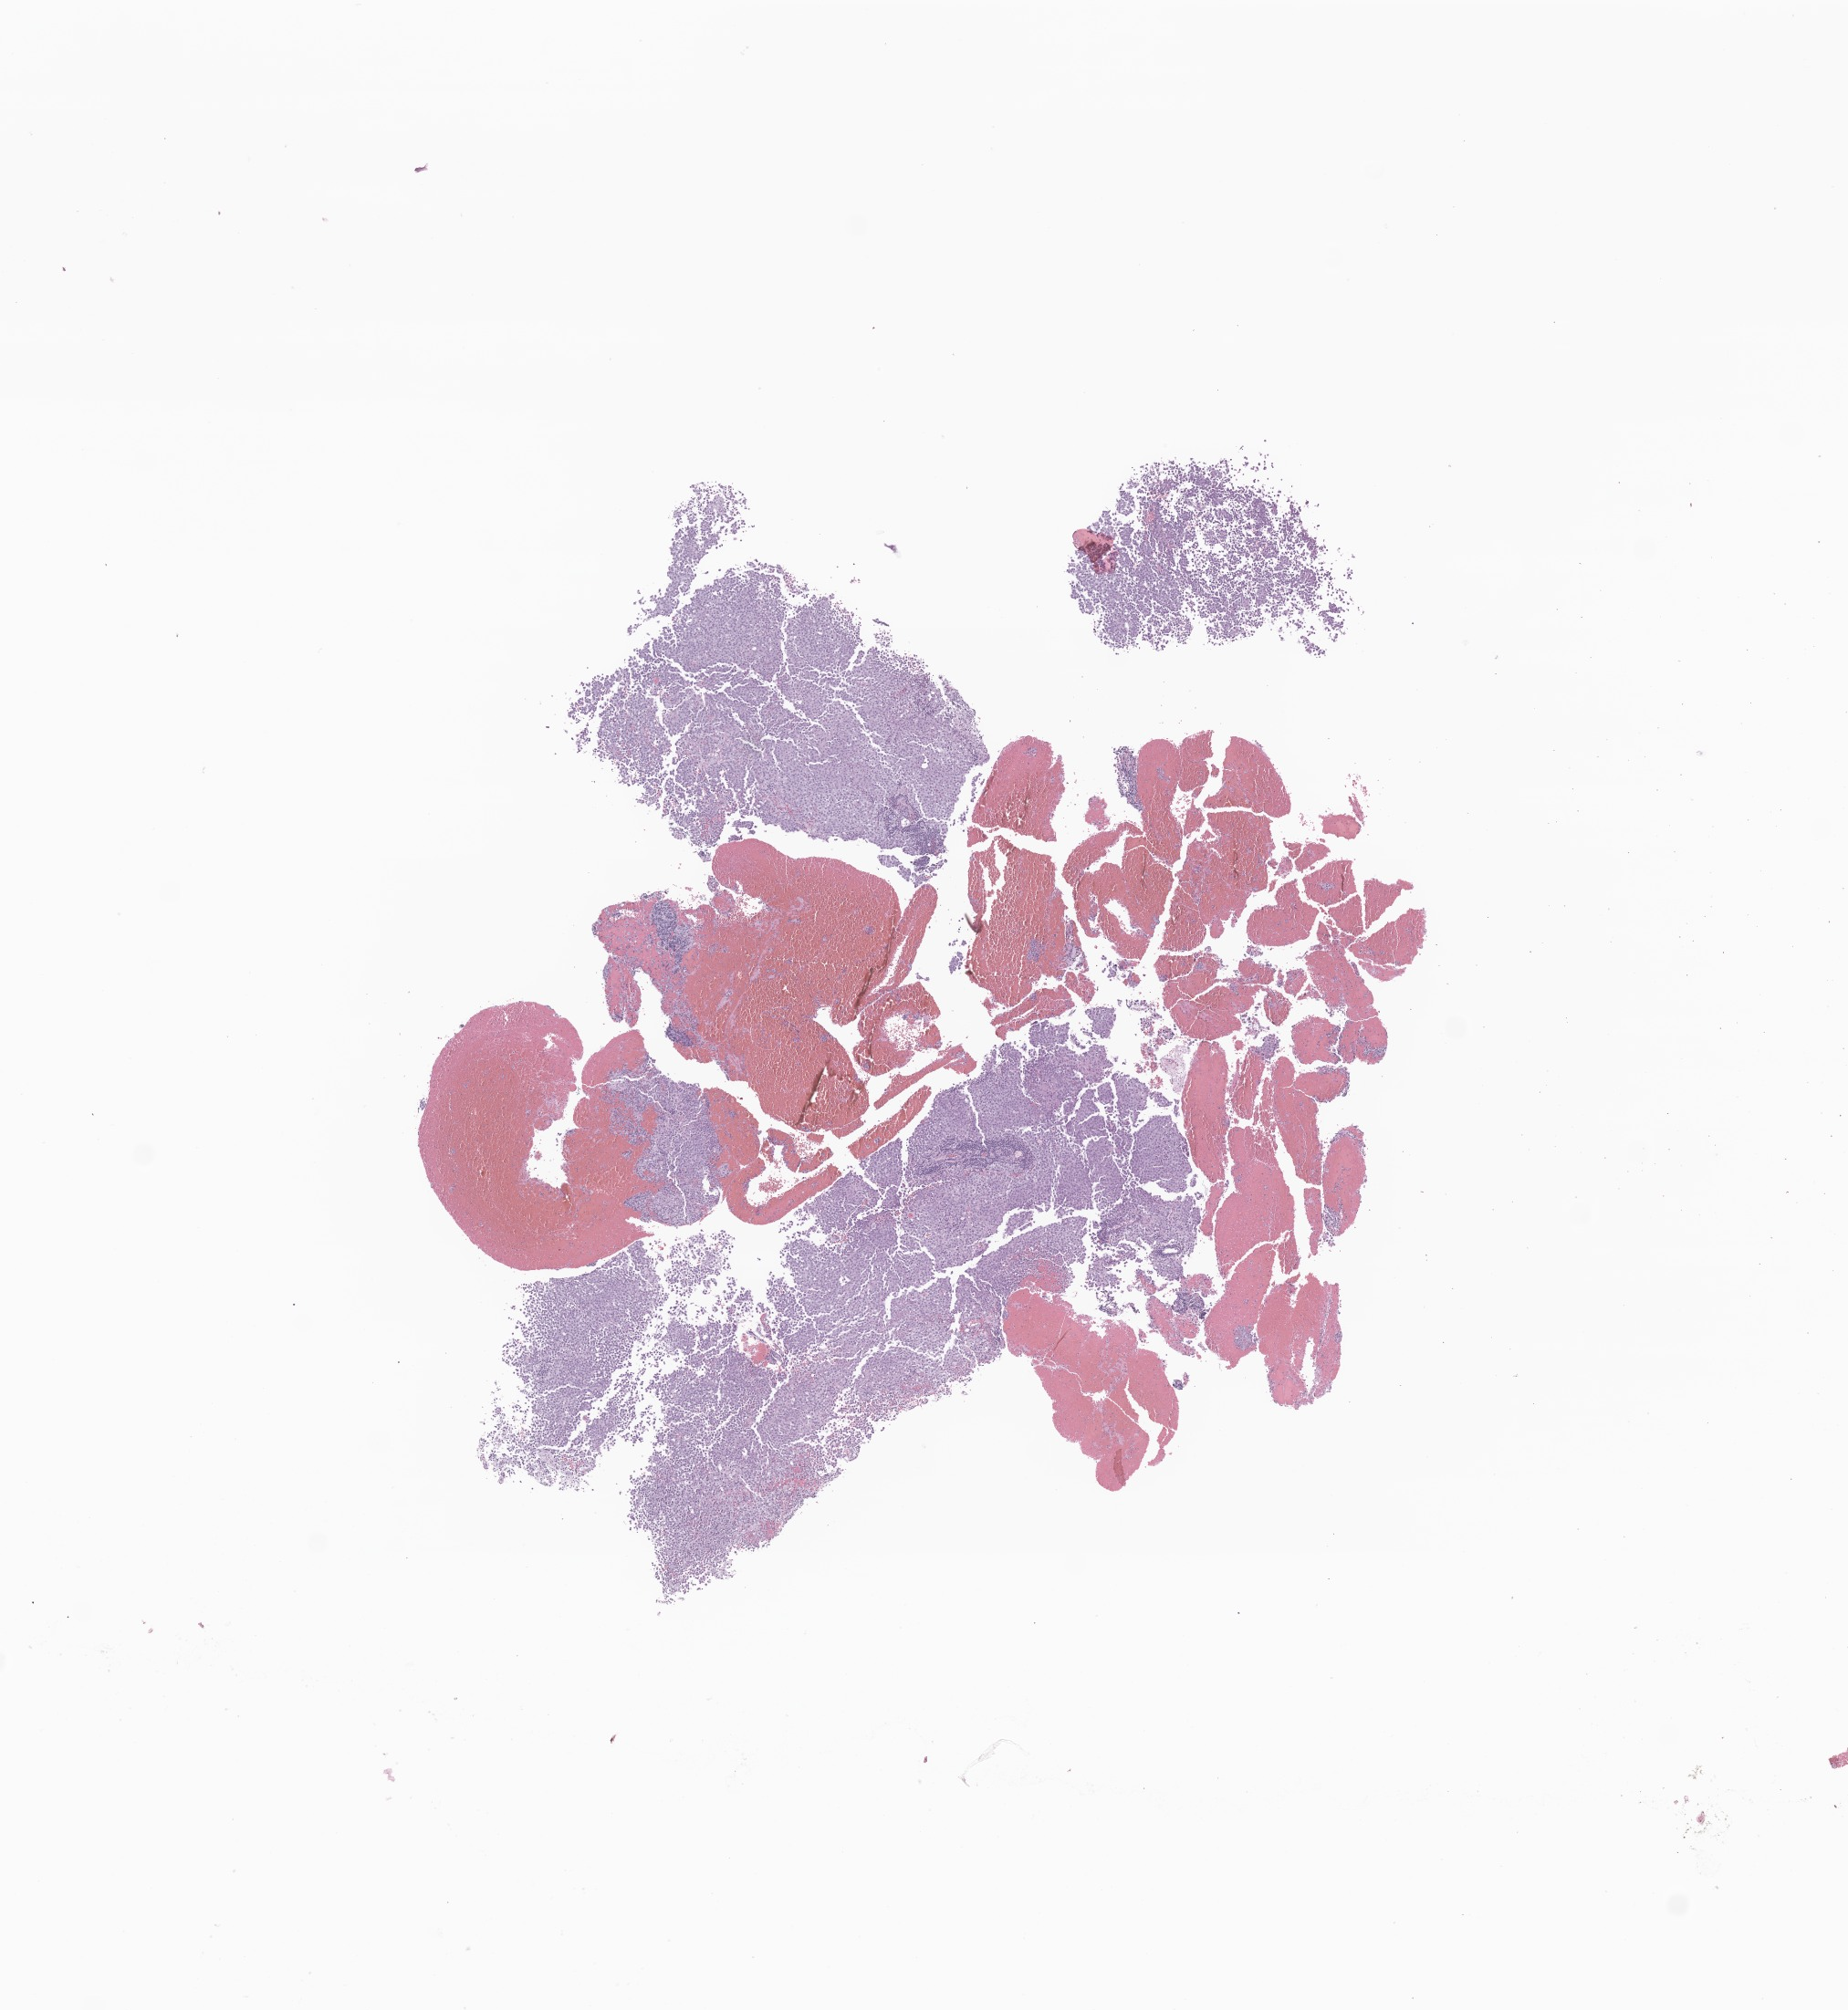
Whole-slide image, hematoxylin and eosin (H&E) stain of tumor tissue from the brain, a low-resolution overview of the entire scanned area, about 8.5 x 9.3 mm, formalin-fixed, paraffin-embedded (FFPE) tissue. Male patient, age 269 months (22 years 5 months).
Diagnosis: Germinoma.